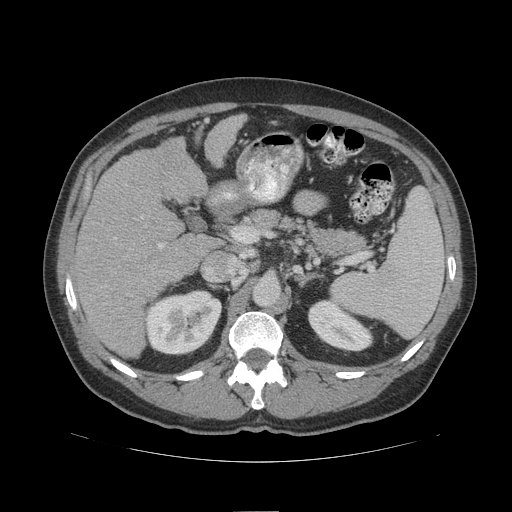
Contrast-enhanced abdominal CT (liver protocol), one axial slice. Position 59 of 109 along the scan axis. Reconstruction kernel STANDARD. 140 kVp. Soft-tissue window (W 400 / L 40 HU). 512 × 512 image matrix, field of view 420 × 420 mm. From the clinical record (not read from this slice): diagnosis: hepatocellular carcinoma (patient treated with transarterial chemoembolisation; whether this scan precedes or follows treatment is not stated here); TNM stage (as recorded): Stage-IIIB; Child-Pugh class: A; tumour differentiation: poorly differentiated.
Annotated regions visible in this slice (semi-automatic segmentation, software-assisted and operator-edited):
- liver parenchyma outside the tumour (the mass and vessels are separate outlines, so this box may not span the whole liver): bounding box <74,114,246,358> (left, top, right, bottom; pixels)
- liver vessels: <158,244,163,248>